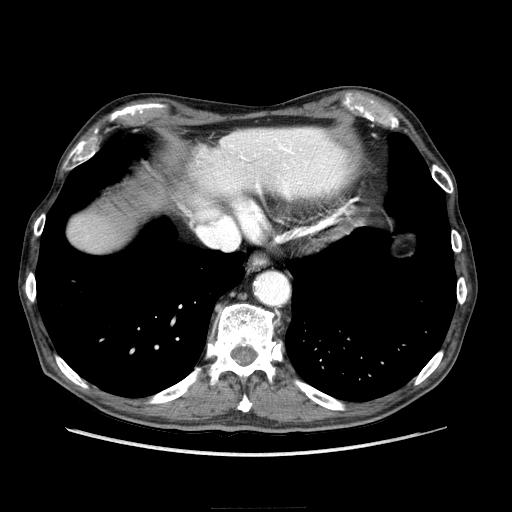
Contrast-enhanced abdominal CT (liver protocol), one axial slice; slice 193 of 218 in the series (ordered by position); reconstruction kernel STANDARD; 100 kVp; soft-tissue window (W 400 / L 40 HU); 2.5 mm slice thickness; 512 × 512 image matrix, field of view 380 × 380 mm. From the clinical record (not read from this slice): diagnosis: hepatocellular carcinoma (patient treated with transarterial chemoembolisation; whether this scan precedes or follows treatment is not stated here); TNM stage (as recorded): Stage-IIIA; Child-Pugh class: A; tumour differentiation: well differentiated; tumour nodularity: multinodular.
Structures marked on this image (semi-automatic segmentation, software-assisted and operator-edited):
- liver parenchyma outside the tumour (the mass and vessels are separate outlines, so this box may not span the whole liver): bounding box <68,214,120,252> (left, top, right, bottom; pixels)